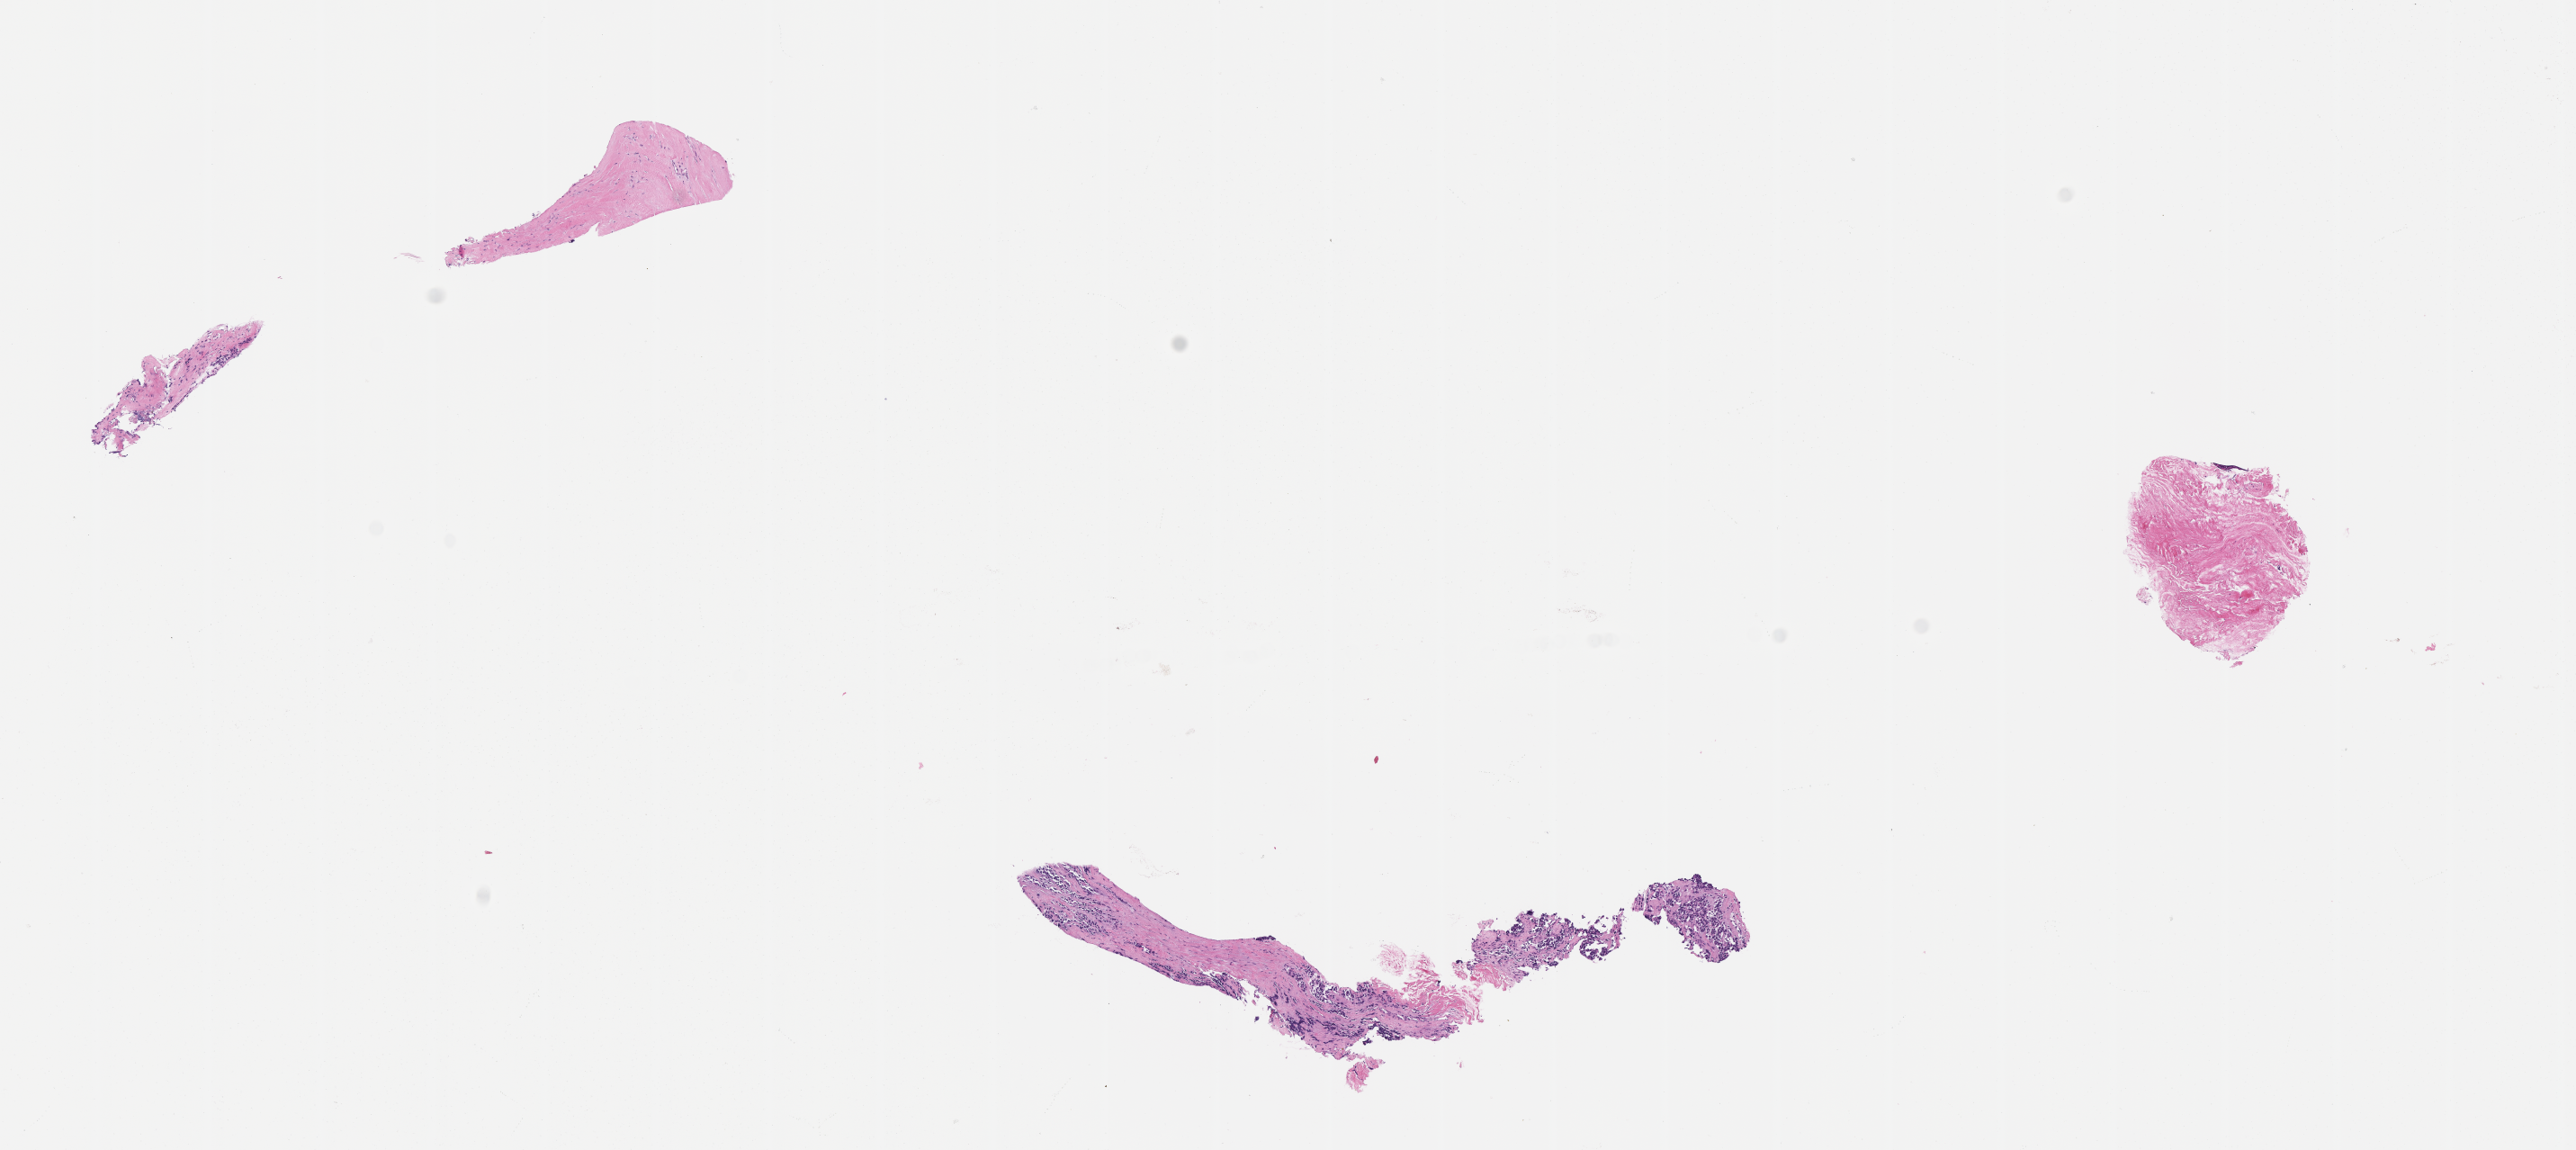
Whole-slide image, haematoxylin and eosin stain of tumor tissue, whole scanned area (about 11.6 x 5.2 mm) shown as a low-resolution overview, formalin-fixed, paraffin-embedded (FFPE) tissue, sample anatomic site: leg-left. Female patient, age at diagnosis 9.6 years.
Diagnosis: rhabdomyosarcoma; histological classification: rhabdomyosarcoma nos.